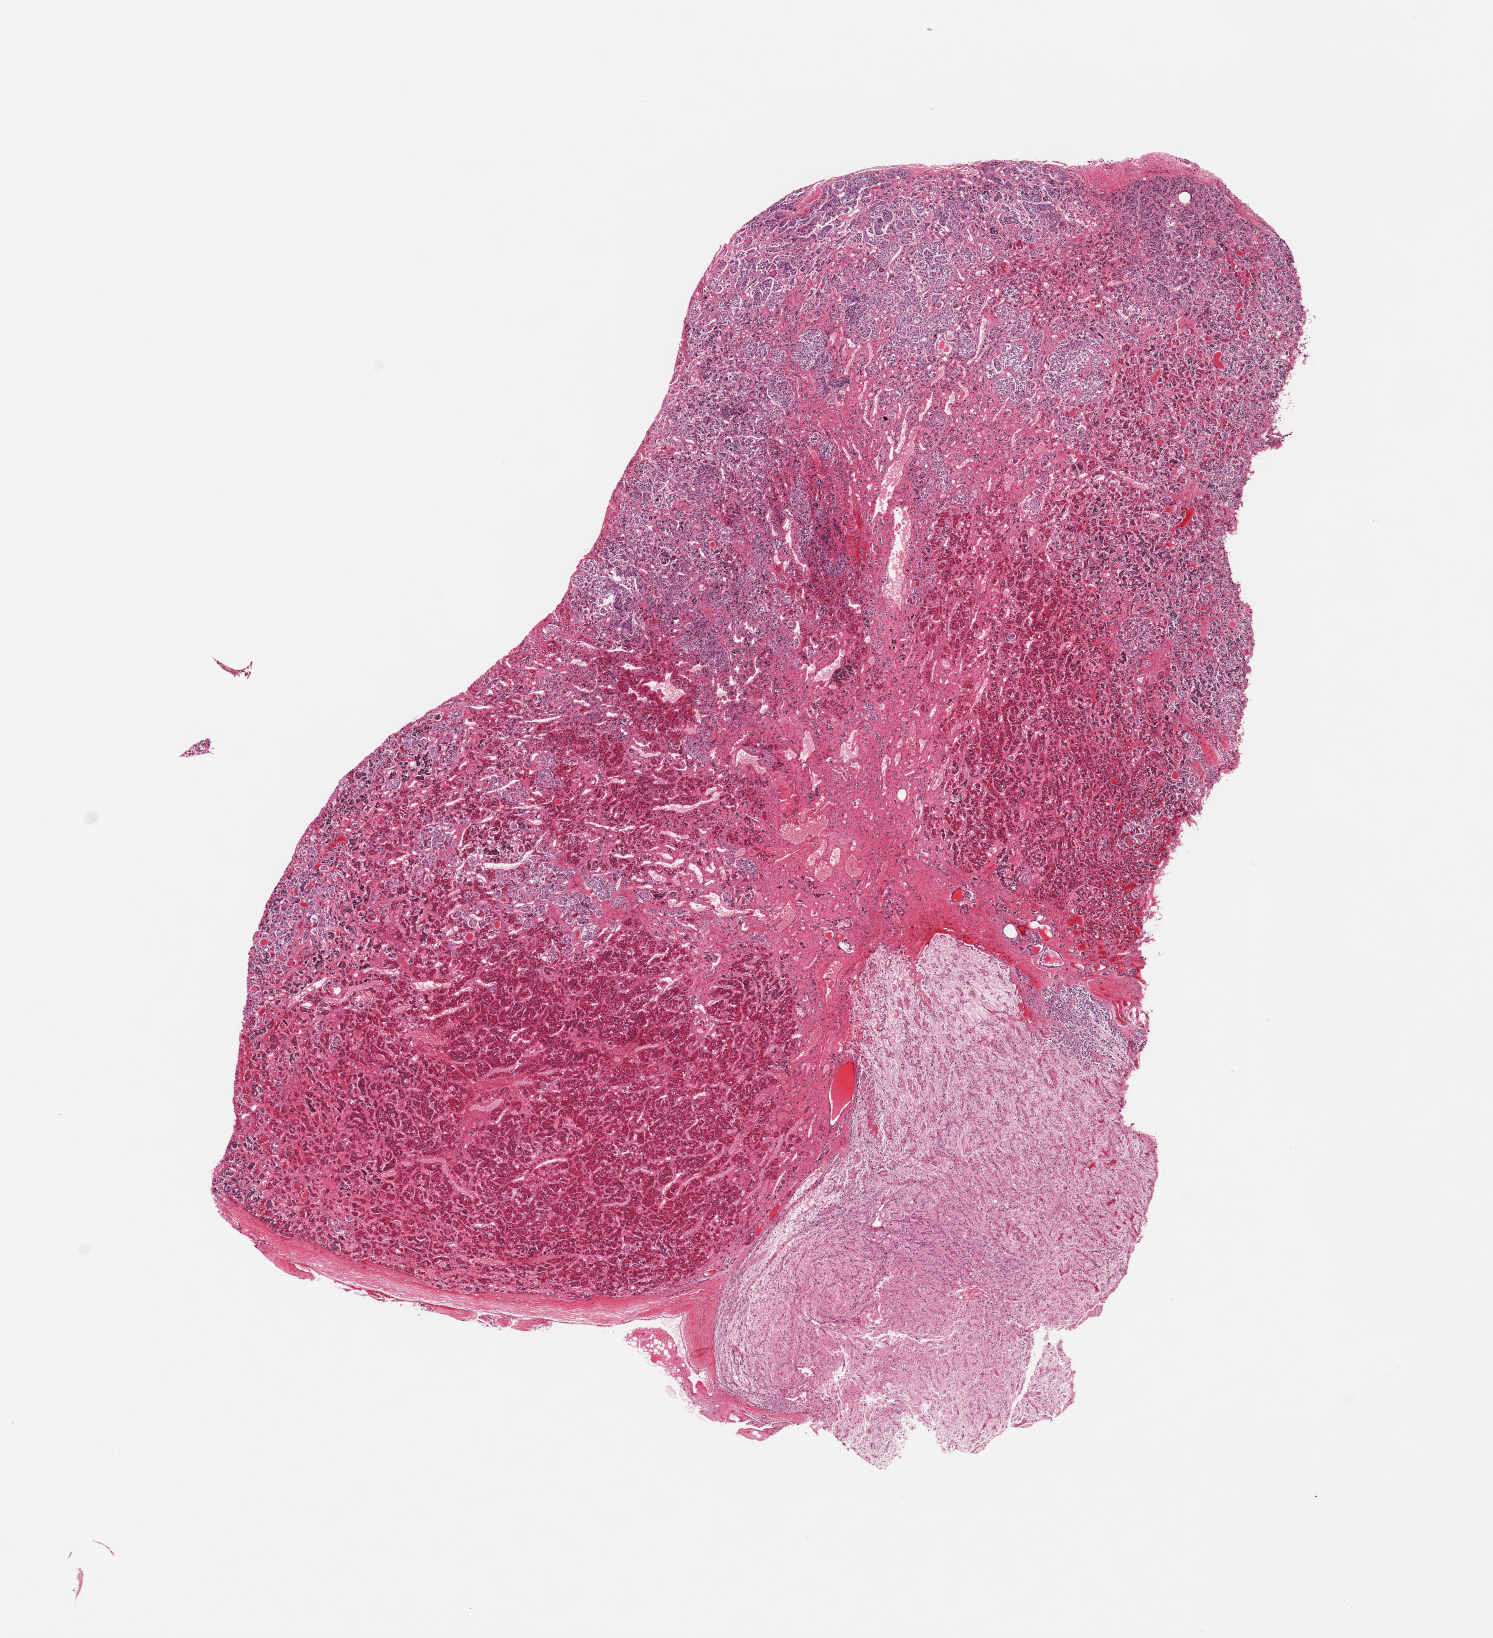
H&E whole-slide image, shown as a low-resolution overview of the whole scanned area (about 11.8 x 13.0 mm, slide scanned at 20x); PAXgene-fixed, paraffin-embedded tissue; target tissue: pituitary; tissue donor sample.
Review note (as recorded): 1 piece; posterior lobe comprises 20% of area.